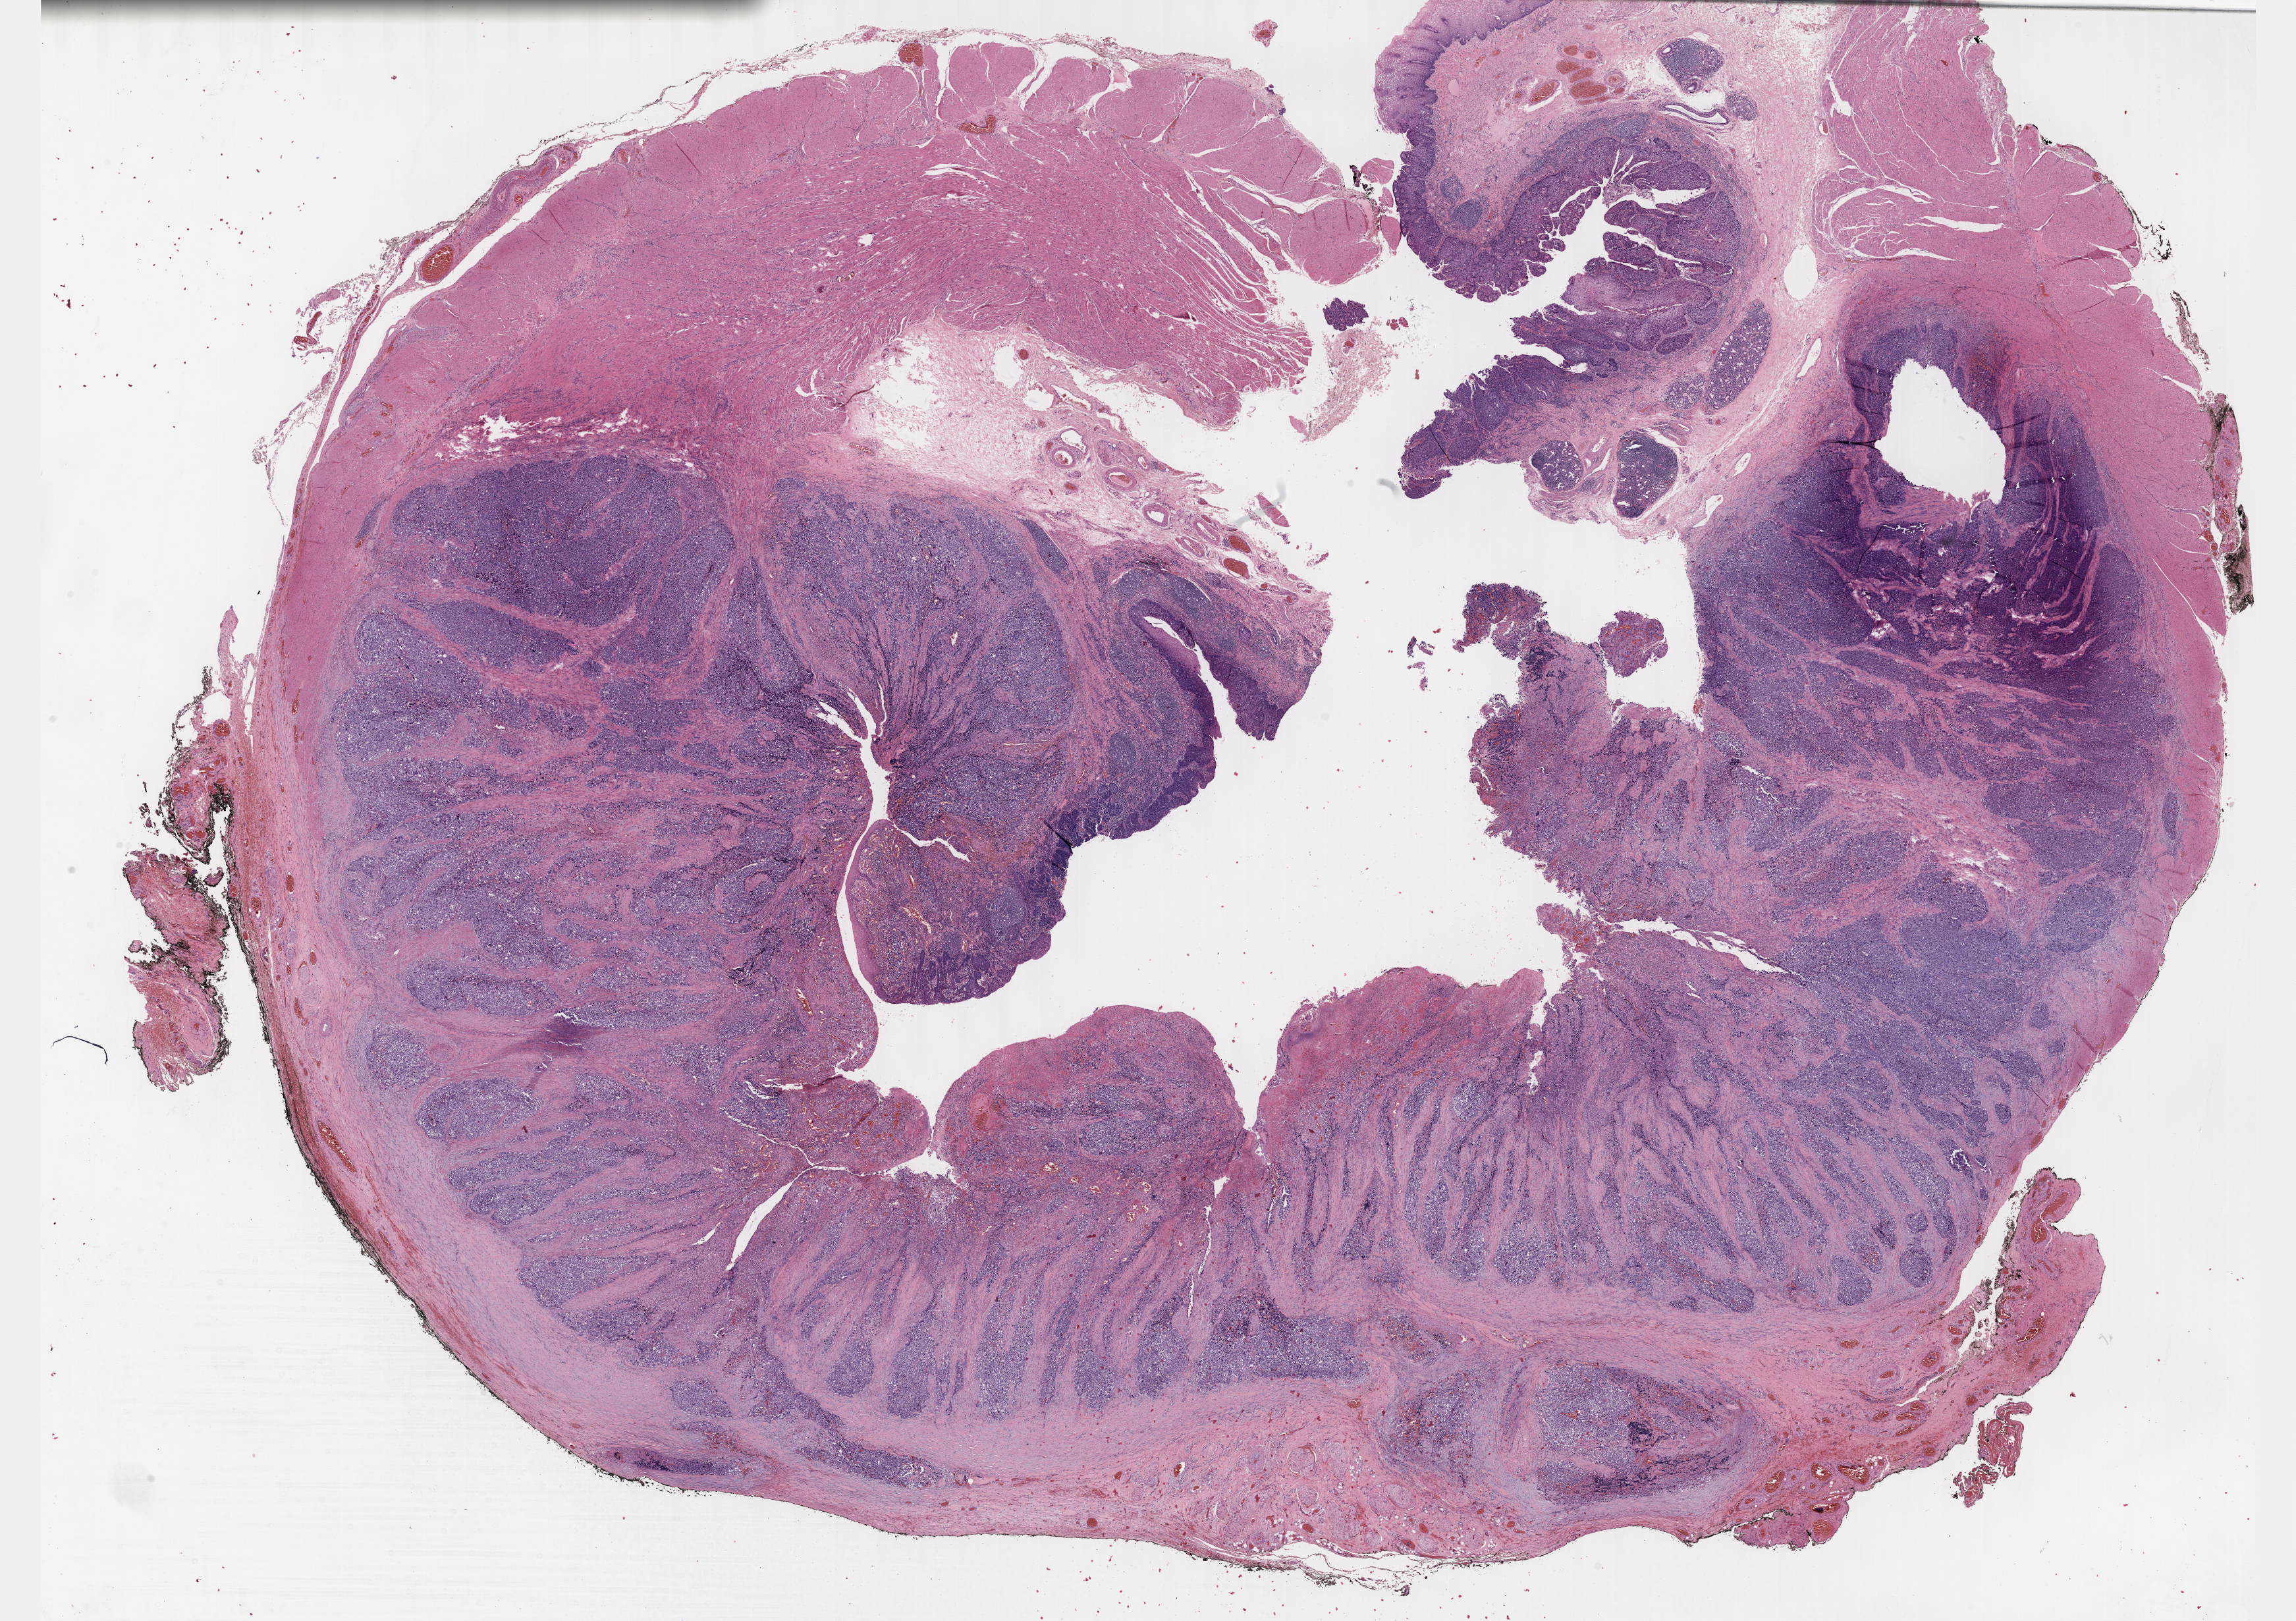
Digitized H&E-stained tissue section (whole slide) — whole scanned area (about 28.2 x 19.9 mm, acquisition: 40x scan) shown as a low-resolution overview; formalin-fixed paraffin-embedded (FFPE) diagnostic section; primary tumour sample from the esophagus. Patient: male, age at initial diagnosis 49 years. Histologic grade: G3 (poorly differentiated).
- AJCC pathologic stage: IIA (7th edition)
- histologic diagnosis: Squamous cell carcinoma, NOS (lower third of esophagus)
- lymph nodes positive (case pathology): 0 of 8 examined